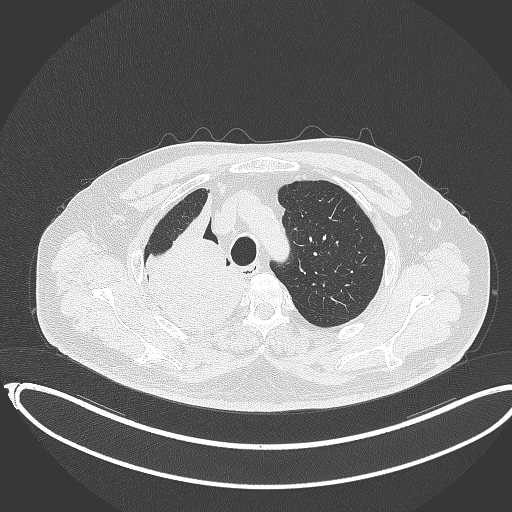
Chest CT, one axial slice; reconstruction kernel B70f; 120 kVp; lung window (W 1500 / L -600 HU); 512 × 512 image matrix. Patient: male, 68 years. From the clinical record (not read from this slice): clinical TNM (as recorded): T2a N0 M0.
Outlined on this slice (bounding box drawn by a radiologist):
- lung tumour (recorded histology: adenocarcinoma): box from (x=137, y=200) to (x=244, y=334) px